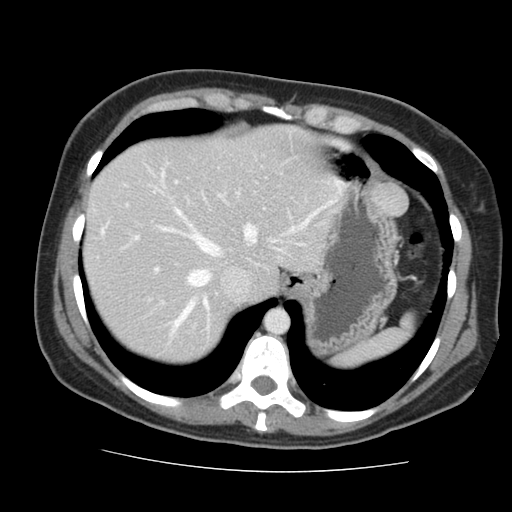
Contrast-enhanced abdominal CT, one axial slice. Slice 122 of 144 in the series (ordered by position). 120 kVp. Intravenous contrast given. Soft-tissue window (W 400 / L 40 HU). 2.5 mm slice thickness. 512 × 512 image matrix, field of view 333 × 333 mm. Female patient, age 46 years. Case-level facts recorded for this patient, not image findings: diagnosis: colorectal cancer liver metastases, imaged before liver resection; multiple liver metastases: no; largest metastasis: 2.8 cm; disease in both lobes: no.
Annotated regions visible in this slice (expert manual segmentation):
- hepatic veins: box from (x=160, y=172) to (x=342, y=335) px
- liver: (x=85, y=128)–(x=336, y=363)
- planned liver remnant (the part of the liver to remain after resection): (x=85, y=128)–(x=336, y=363)
- portal vein (with intrahepatic branches): (x=102, y=231)–(x=158, y=272)